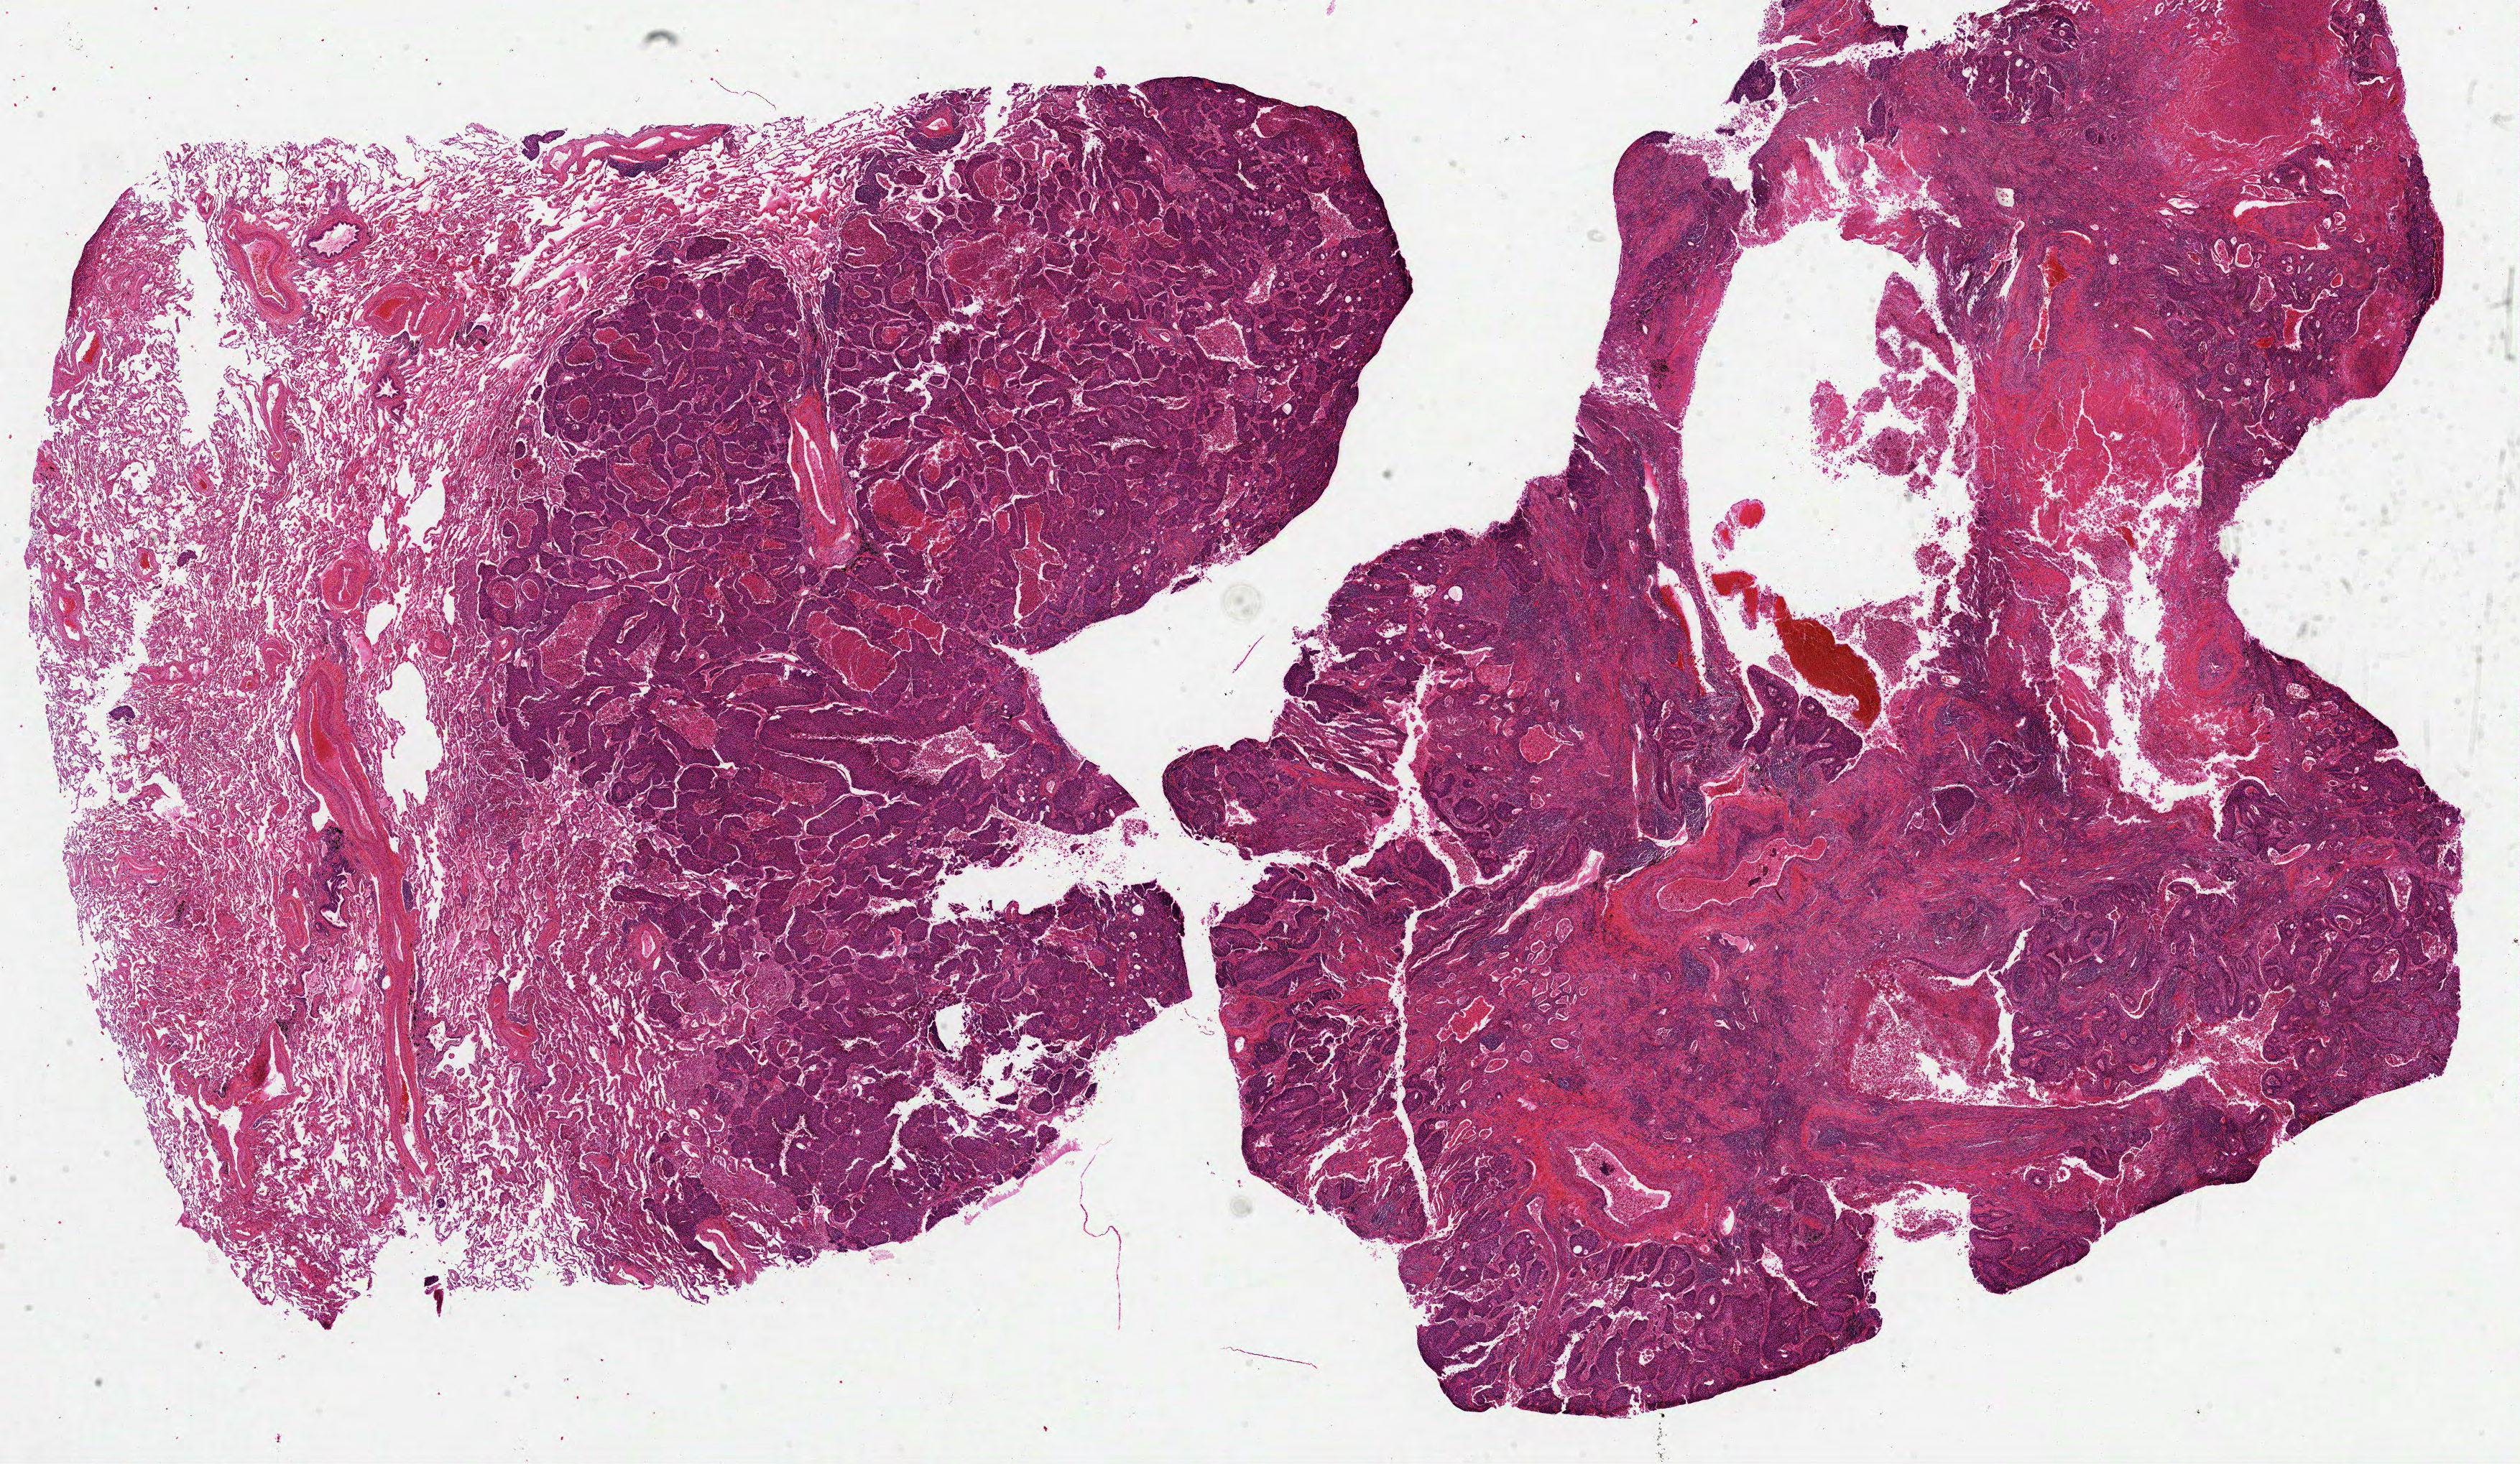
H&E-stained whole-slide image, shown as a low-resolution overview of the whole scanned area (about 28.3 x 16.4 mm). Formalin-fixed paraffin-embedded (FFPE) diagnostic section. Lung, primary tumour sample. Patient: male, age at initial diagnosis 68 years.
AJCC pathologic stage: IB (5th edition). TNM: T2 N0 M0. Diagnosis: Squamous cell carcinoma, NOS (lower lobe, lung).